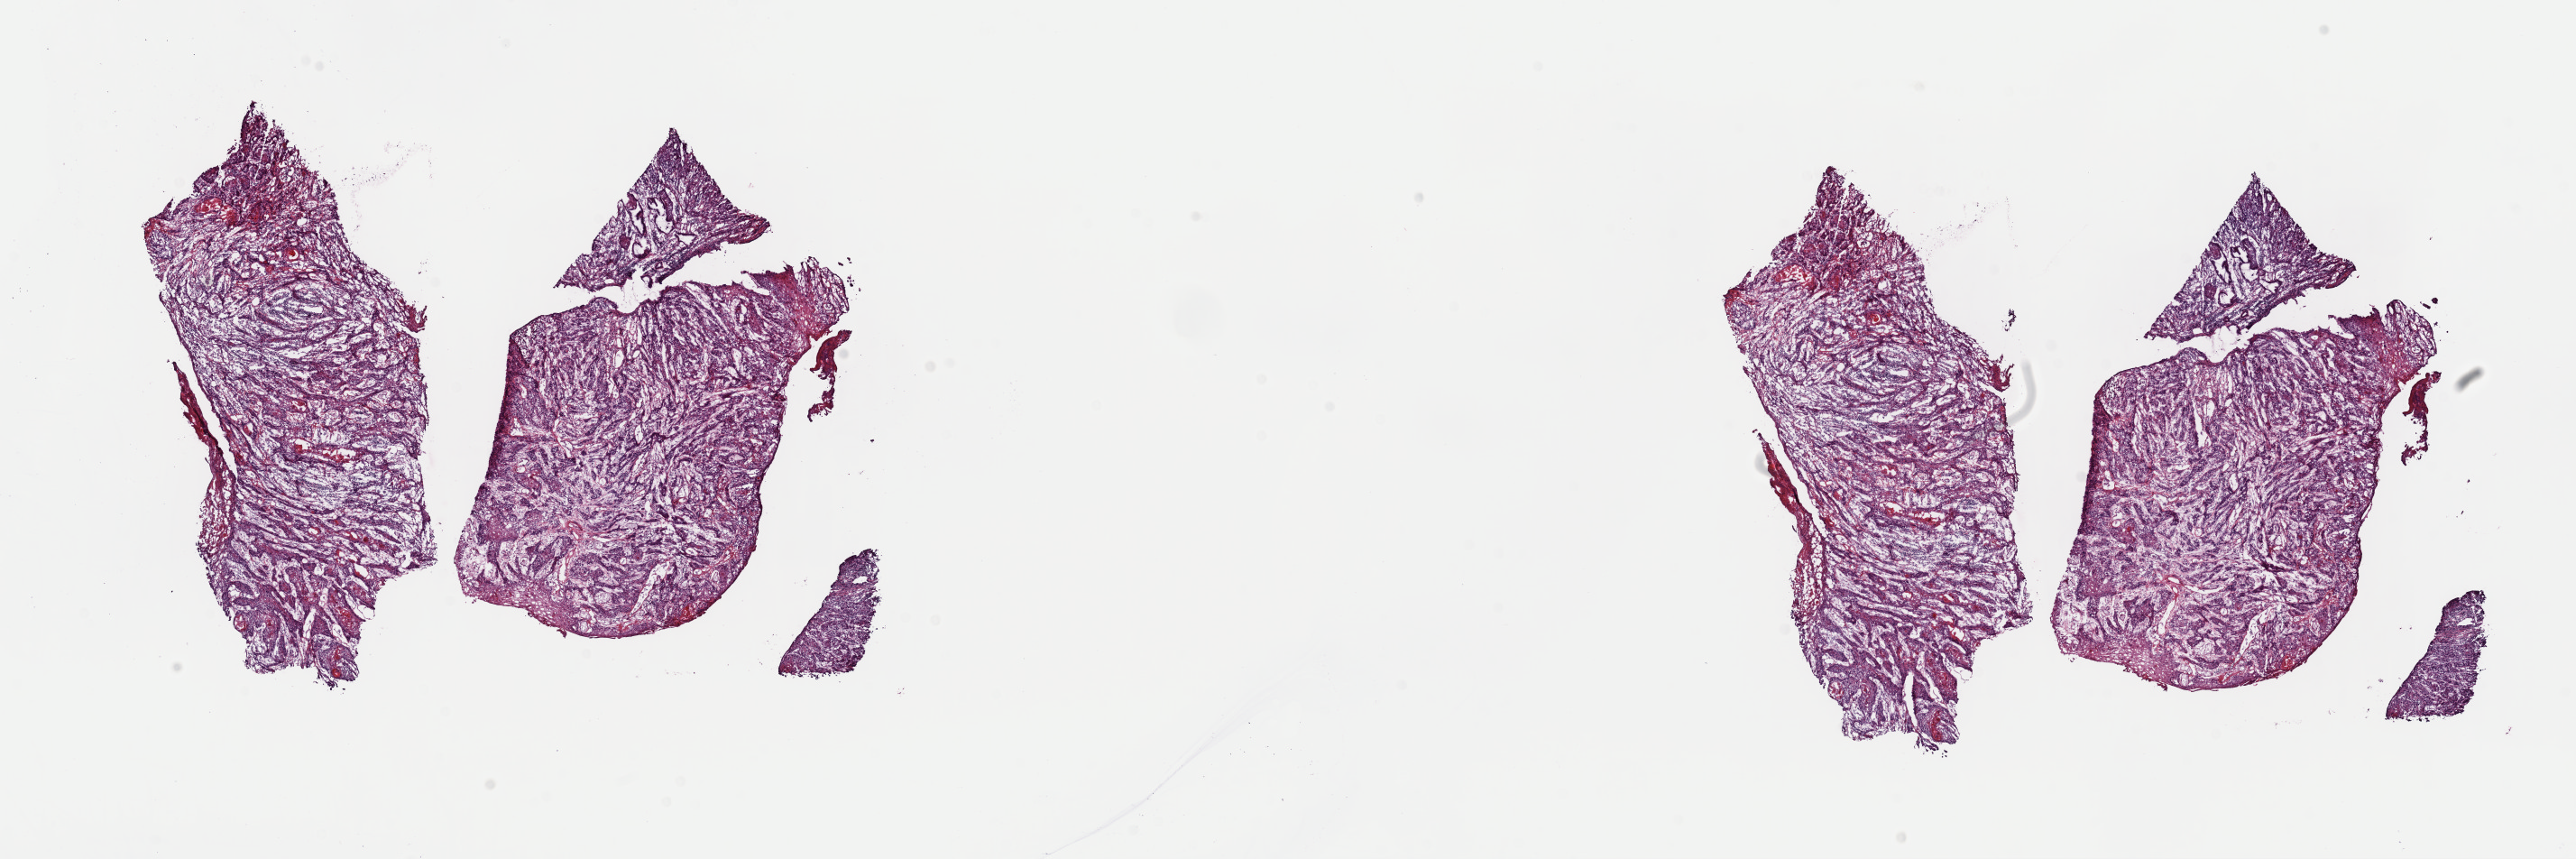
Digitized H&E-stained tissue section (whole slide), low-resolution overview of the scanned area, about 22.6 x 7.5 mm (from a 40x scan). Frozen section from the top of the tissue portion. Head and neck, primary tumour sample. Female patient; age at initial diagnosis 52 years. Histologic grade: G2 (moderately differentiated). Slide review estimates, as recorded: tumour cells 80%, tumour nuclei 90%, normal cells 0%, stromal cells 20%, necrosis 0%. Infiltration values recorded for this section: lymphocyte infiltration 3%, monocyte infiltration 0%, neutrophil infiltration 0%.
AJCC pathologic stage: I. Histologic diagnosis: Squamous cell carcinoma, NOS (tongue, NOS). Laterality: left.